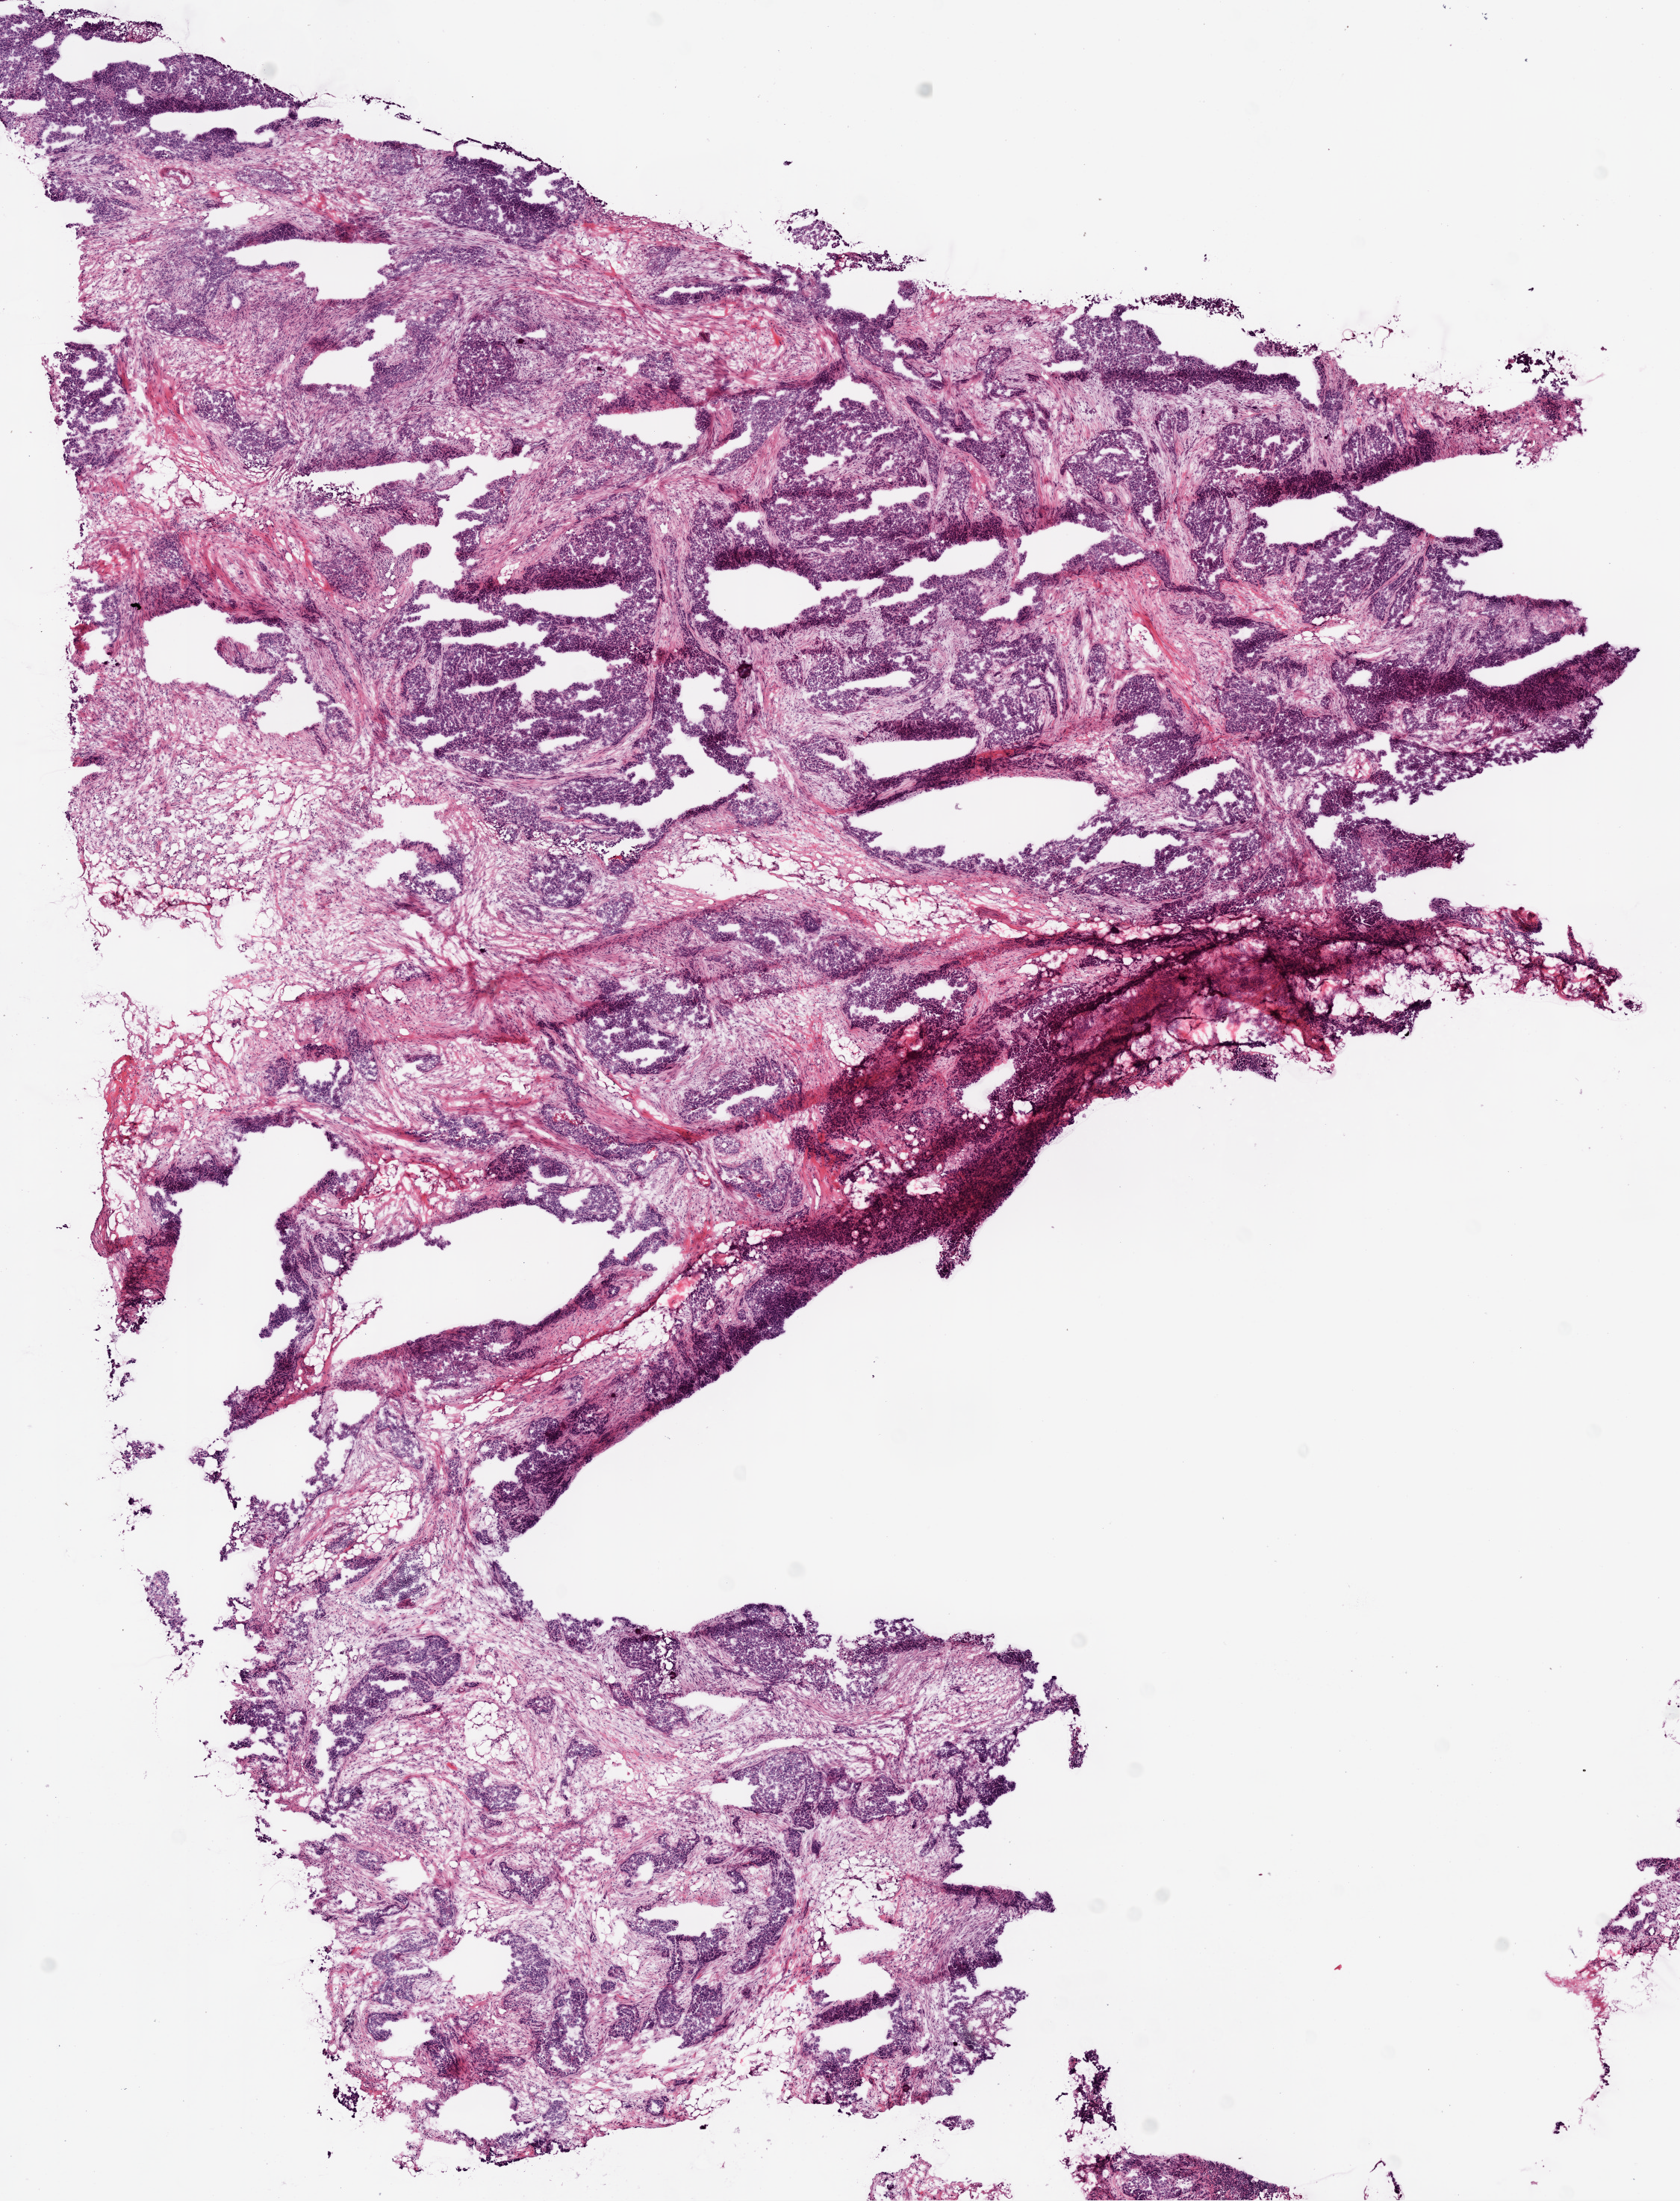
H&E whole-slide image — shown as a low-resolution overview of the whole scanned area (about 9.0 x 11.8 mm). Frozen section from the bottom of the tissue portion. Ovary, primary tumour sample. Patient: female, age at initial diagnosis 63 years. Histologic grade: G3 (poorly differentiated). Slide review estimates, as recorded: tumour cells 80%, tumour nuclei 80%, normal cells 0%, stromal cells 20%, necrosis 0%.
Histologic diagnosis: Serous cystadenocarcinoma, NOS. FIGO stage: IIIC. Laterality: bilateral.